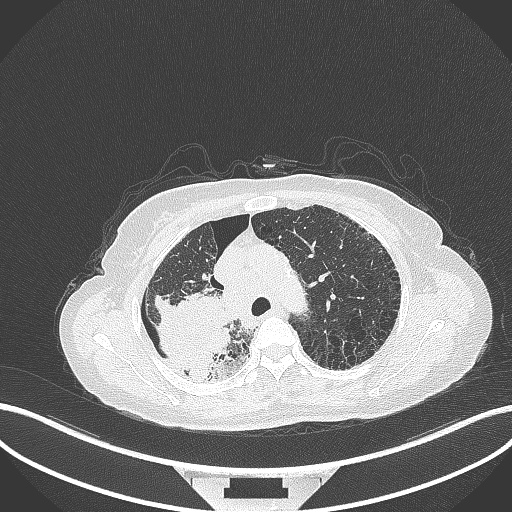
Chest CT, one axial slice. Slice 259 of 408 in the series (ordered by position). 120 kVp. Lung window (W 1500 / L -600 HU). 512 × 512 image matrix, field of view 400 × 400 mm. Patient: female, 64 years. Case-level facts recorded for this patient, not image findings: clinical TNM (as recorded): T3 N3 M0.
Annotated regions visible in this slice (bounding box drawn by a radiologist):
- lung tumour (recorded histology: squamous cell carcinoma): bounding box <144,286,235,381> (left, top, right, bottom; pixels)